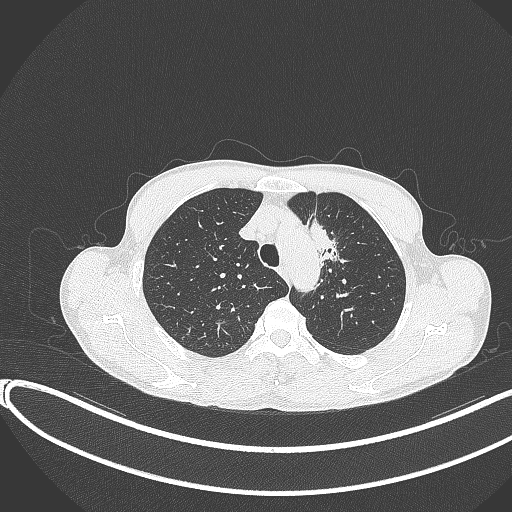
Chest CT, one axial slice. Slice 301 of 374 in the series (ordered by position). 120 kVp. Lung window (W 1500 / L -600 HU). 1 mm slice thickness. 512 × 512 image matrix, field of view 400 × 400 mm. Patient: male, 58 years. Case-level facts recorded for this patient, not image findings: clinical TNM (as recorded): T1c N1 M0.
Outlined on this slice (rectangle marked by the reading radiologist):
- lung tumour (recorded histology: adenocarcinoma): bounding box [x1, y1, x2, y2] px = [307, 212, 360, 282]